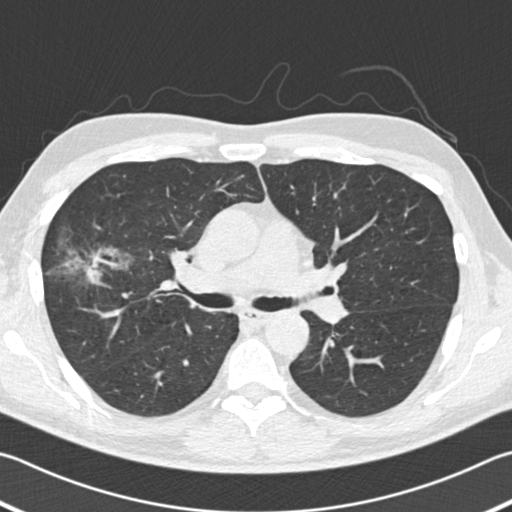
Chest CT (low-dose screening protocol), one axial image, second screening round (one year after baseline), lung window (W 1500 / L -600 HU), standard (soft-tissue) reconstruction kernel (B30f), 120 kVp, slice 68 of 182 in the series, 512 × 512 image matrix, field of view 344 × 344 mm. Male, age 56 years at enrolment. Former smoker at enrolment.
Lesion marked by an expert reader, box from (x=48, y=233) to (x=133, y=298) px. The exam's reader record, not a measurement of the box and not confirmed to be the same lesion: non-calcified nodule or mass ≥4 mm, right upper lobe, 18 × 14 mm, spiculated (stellate) margins, soft tissue attenuation, pre-existing on the prior screen: yes; interval growth: yes.